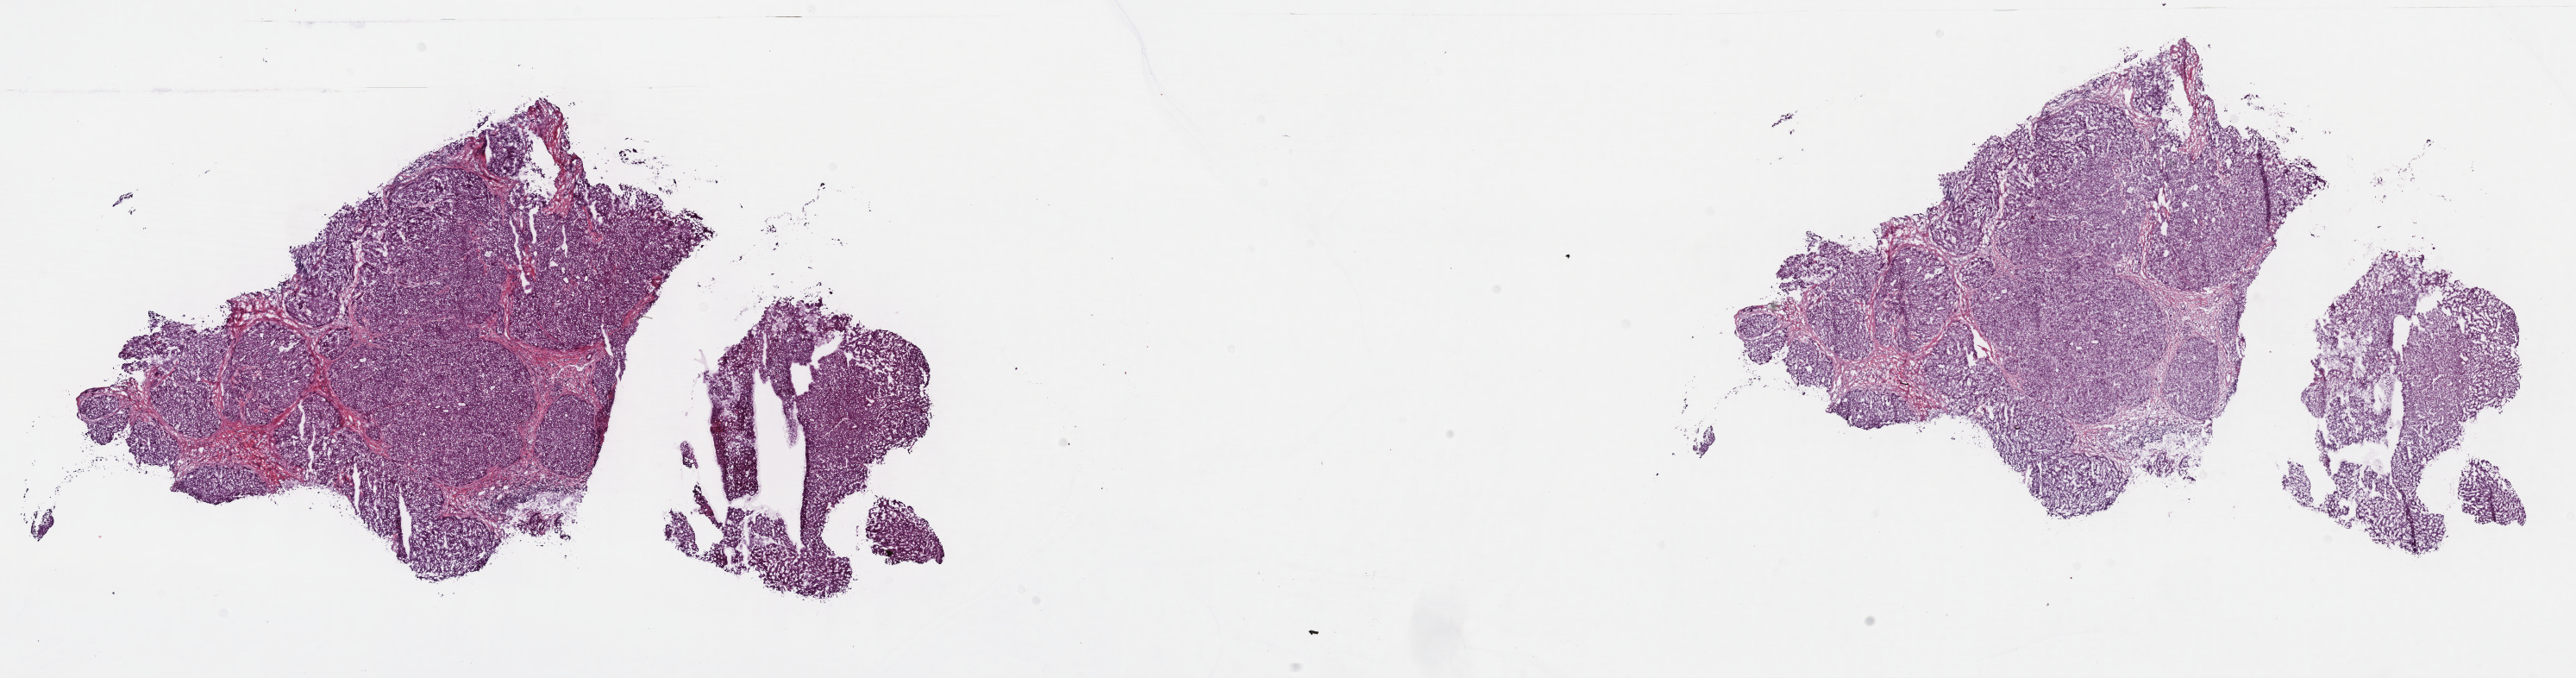
Whole-slide histology image, Hematoxylin and eosin (H&E) stained — whole scanned area (about 24.2 x 6.4 mm, slide scanned at 40x) shown as a low-resolution overview. Frozen section from the top of the tissue portion. Liver, primary tumour sample. Patient: male, age at initial diagnosis 51 years. Histologic grade: G2 (moderately differentiated). Pathologist review of this section (percent, as recorded): tumour cells 80%, tumour nuclei 80%, normal cells 0%, stromal cells 20%, necrosis 0%. Inflammatory infiltration, as recorded: lymphocyte infiltration 3%, monocyte infiltration 1%, neutrophil infiltration 2%.
AJCC pathologic stage: I (6th edition). Histologic diagnosis: Hepatocellular carcinoma, NOS.